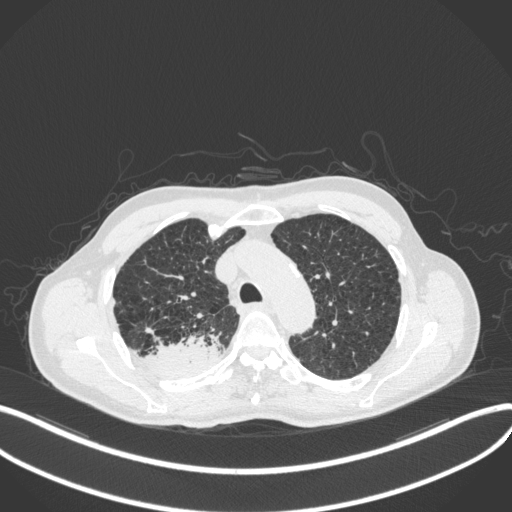
Chest CT, one axial slice. Position 333 of 423 along the scan axis. Reconstruction kernel B31f. 120 kVp. Lung window (W 1500 / L -600 HU). 1 mm slice thickness. 512 × 512 image matrix. Patient: male, 79 years. From the clinical record (not read from this slice): clinical TNM (as recorded): T3 N0 M0.
Annotated regions visible in this slice (rectangle marked by the reading radiologist):
- lung tumour (recorded histology: adenocarcinoma): bounding box <137,332,226,380> (left, top, right, bottom; pixels)